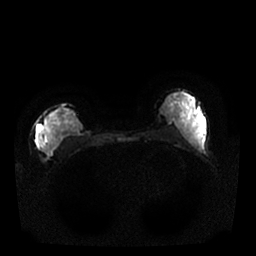
Breast MRI, one axial slice. Position 12 of 25 along the scan axis. Diffusion-weighted series; image 2 of 4 stored at this slice position (different b-values; order by instance number). 1.5 T. 4 mm slice thickness. 256 × 256 image matrix, field of view 340 × 340 mm. Female patient.
Annotated regions visible in this slice (manually delineated by an expert):
- tumour on diffusion-weighted imaging: bounding box [x1, y1, x2, y2] px = [37, 125, 58, 152]